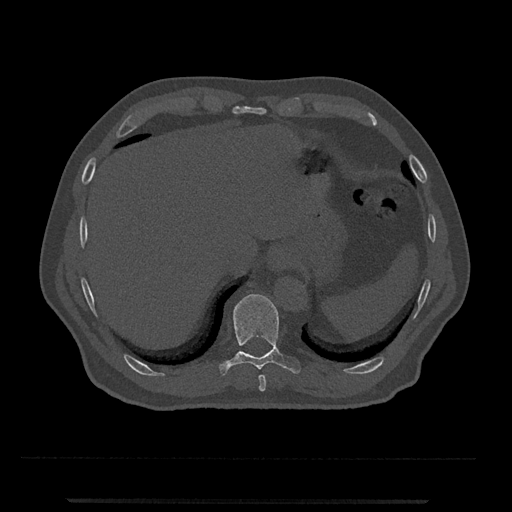
CT including the spine, one axial slice; slice 521 of 797 in the series (ordered by position); reconstruction kernel Br40s/3; 120 kVp; bone window (W 1800 / L 400 HU); 512 × 512 image matrix, field of view 419 × 419 mm. Male patient, age 63 years. Case-level facts recorded for this patient, not image findings: primary cancer: prostate.
Annotated regions visible in this slice (semi-automatic segmentation, software-assisted and operator-edited):
- T10 vertebra: bounding box (x1, y1, x2, y2) in pixels: (220, 294, 301, 375)
- T9 vertebra: (259, 375, 266, 392)